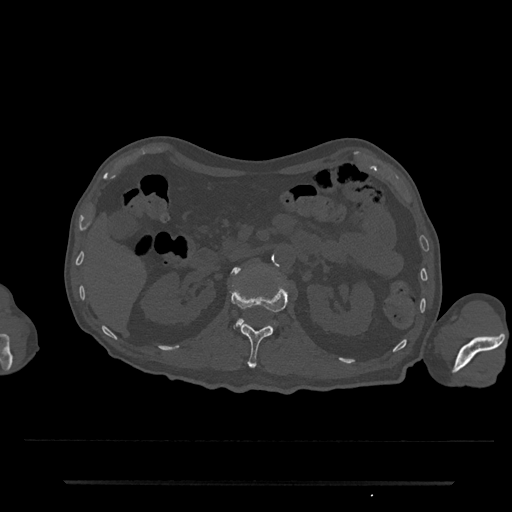
CT including the spine, one axial slice; slice 110 of 797 in the series (ordered by position); reconstruction kernel Br40s/3; 120 kVp; bone window (W 1800 / L 400 HU); 512 × 512 image matrix, field of view 427 × 427 mm. Male patient, age 74 years. From the clinical record (not read from this slice): primary cancer: prostate.
Annotated regions visible in this slice (semi-automatically segmented with operator editing):
- L1 vertebra: bounding box (x1, y1, x2, y2) in pixels: (231, 284, 288, 368)
- L2 vertebra: (234, 267, 243, 326)